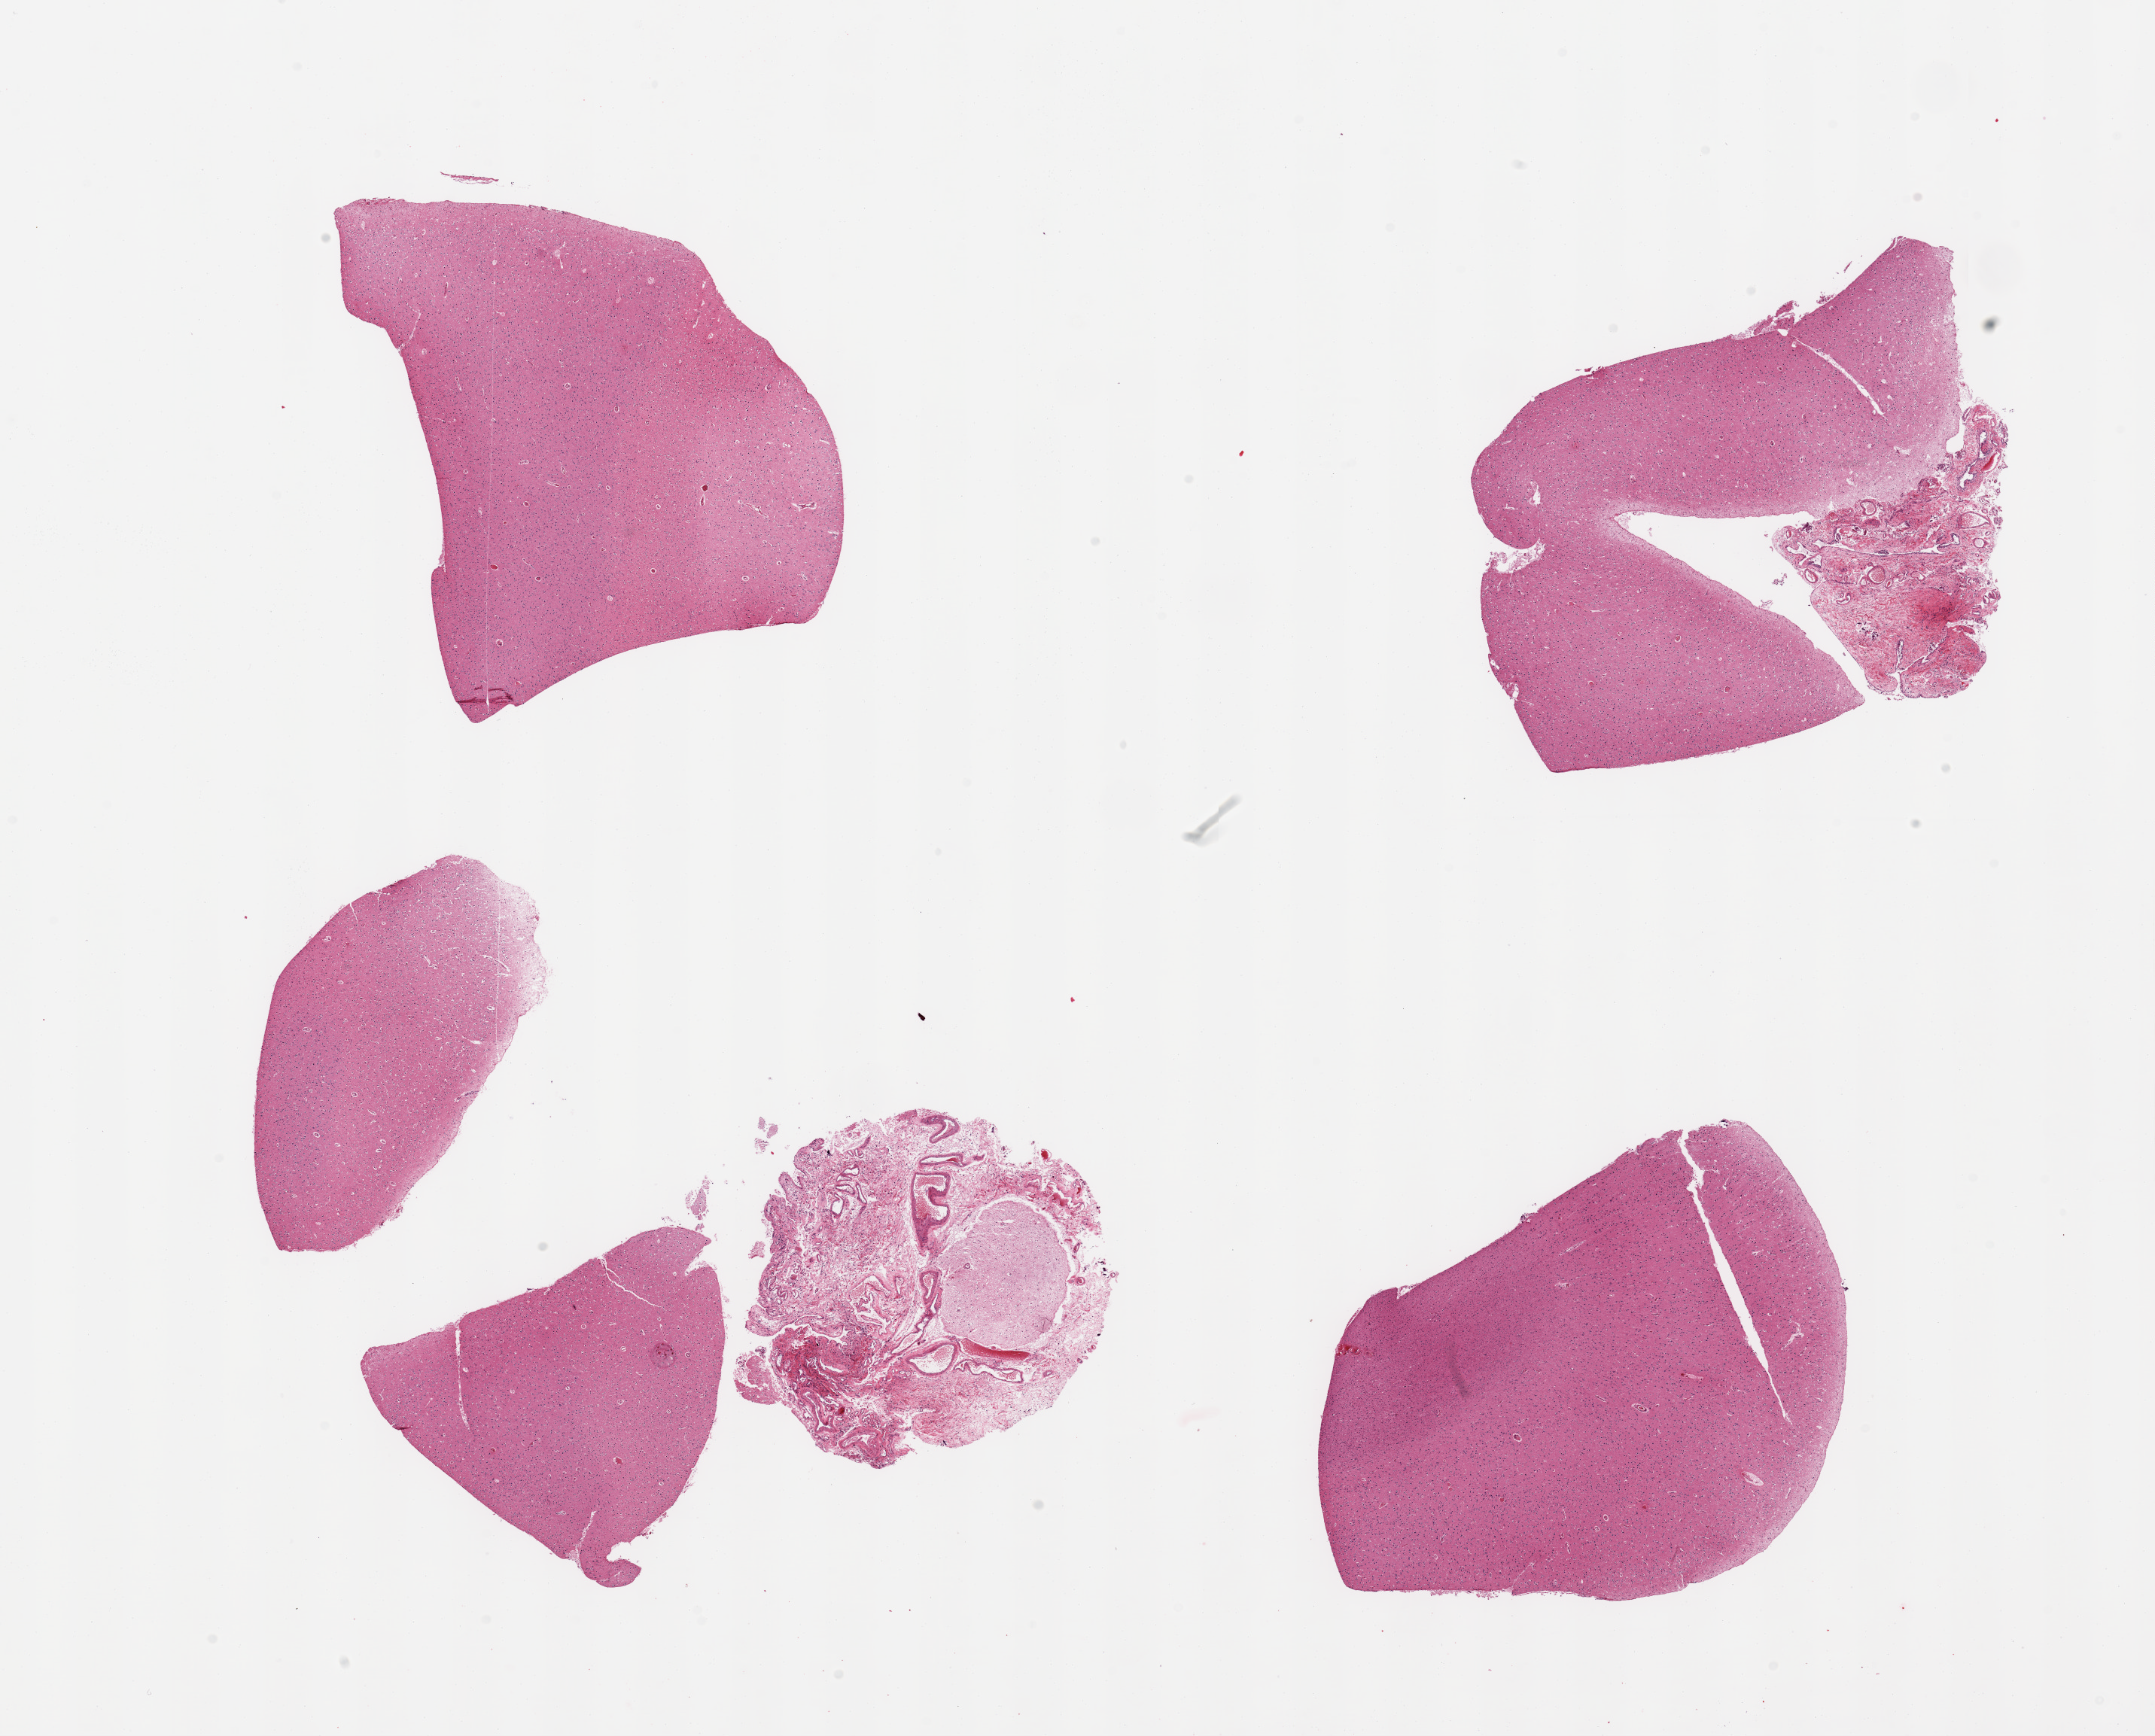
Digitized hematoxylin and eosin (H&E)-stained section — low-resolution overview of the scanned area, about 22.6 x 18.2 mm (slide scanned at 20x); PAXgene-fixed paraffin-embedded (PFPE) section; sampled site (target tissue): cerebral cortex; tissue donor sample. Donor sex: female.
Pathologist's review note for this sample: 4 pieces, no abnormalities, separate fragment of dura.